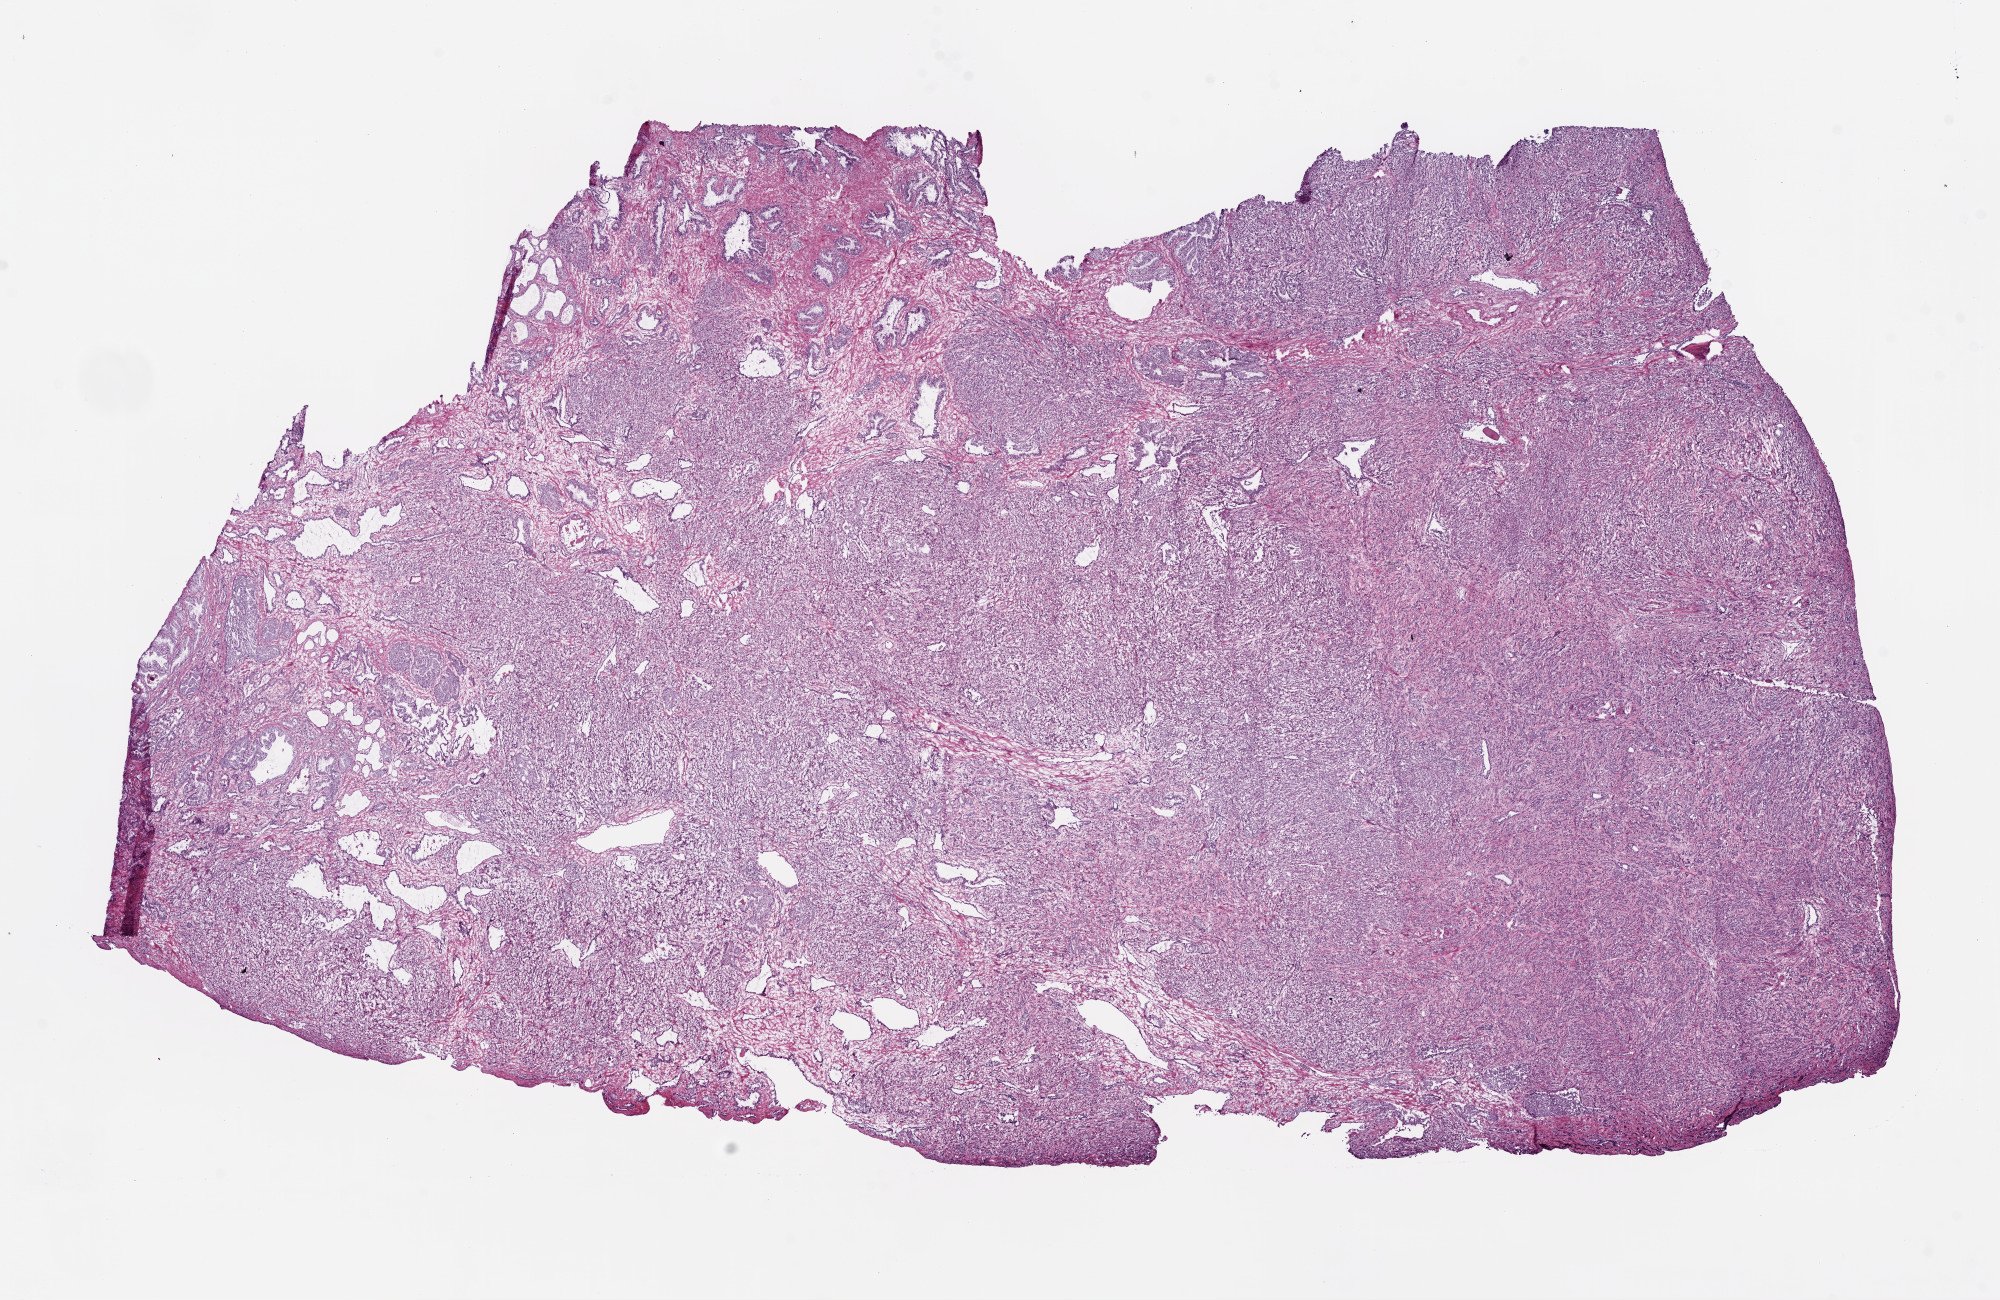
Digitized H&E-stained tissue section (whole slide) — low-resolution overview of the scanned area, about 16.0 x 10.4 mm; frozen section from the bottom of the tissue portion; prostate, primary tumour sample. Patient: male, age at initial diagnosis 56 years. Gleason score: 8 (4+4). Pathologist review of this section (percent, as recorded): tumour cells 80%, tumour nuclei 80%, normal cells 5%, stromal cells 15%, necrosis 0%. Infiltration values recorded for this section: lymphocyte infiltration 2%, monocyte infiltration 0%, neutrophil infiltration 0%.
• histologic diagnosis: Acinar cell carcinoma (prostate gland)
• lymph nodes positive (case pathology): 1 of 27 examined